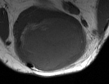
MRI of an extremity soft-tissue mass, one axial slice. Position 26 of 50 along the scan axis. MR volume resampled by the dataset authors to the PET/CT grid (not the native acquisition matrix). 109 × 84 image matrix, field of view 106 × 82 mm. Male patient. Case-level facts recorded for this patient, not image findings: histological type: synovial sarcoma; site of the primary tumour: left poplietal fossa.
Annotated regions visible in this slice (expert contour drawn on MRI and transferred to this co-registered scan by the dataset authors):
- gross tumour volume (mass): bounding box [x1, y1, x2, y2] px = [14, 14, 86, 72]